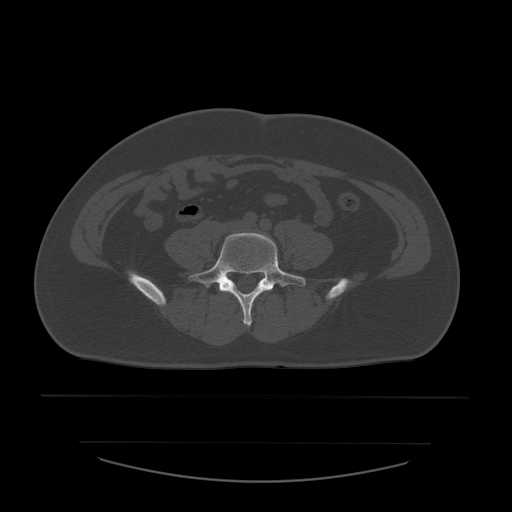
CT including the spine, one axial slice; slice 124 of 532 in the series (ordered by position); bone window (W 1800 / L 400 HU); 512 × 512 image matrix, field of view 441 × 441 mm. Patient age 44 years. Case-level facts recorded for this patient, not image findings: primary cancer: soft tissue sarcoma.
Structures marked on this image (semi-automatically segmented with operator editing):
- L5 vertebra: box from (x=188, y=233) to (x=306, y=326) px